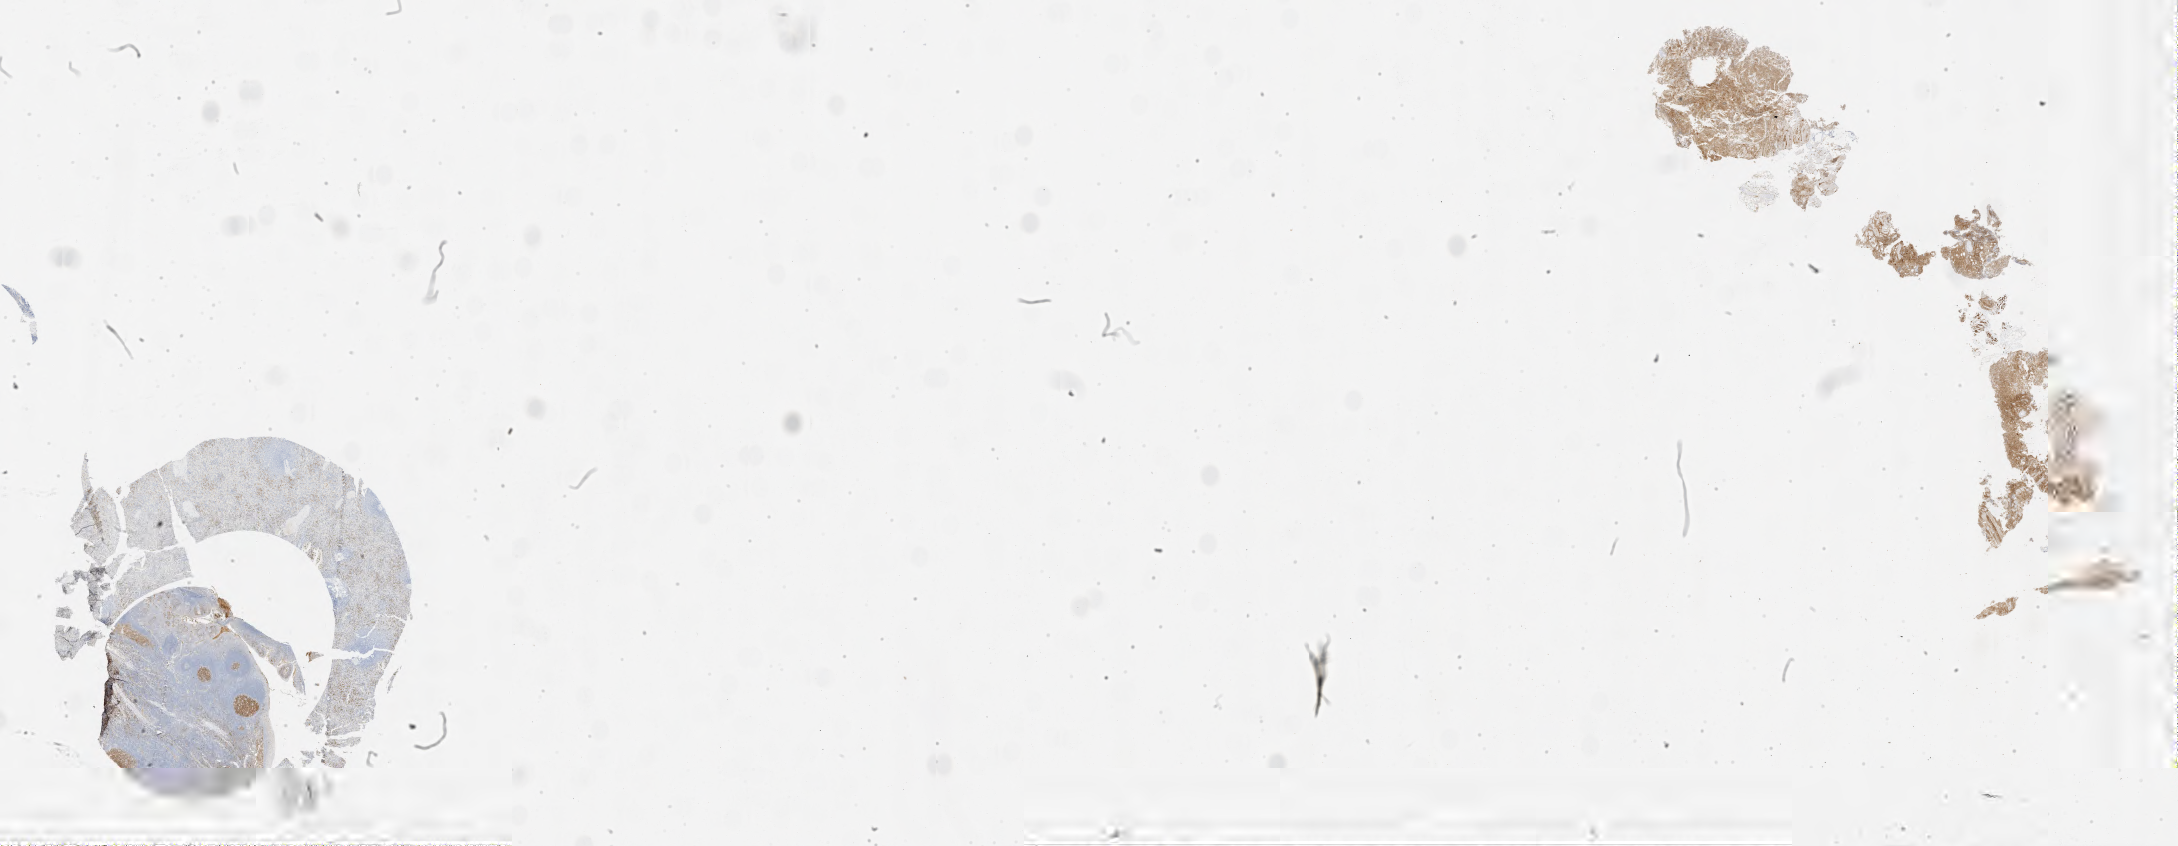
Whole-slide image, immunohistochemical stain for CD10 — whole scanned area (about 35.0 x 13.6 mm) shown as a low-resolution overview, specimen: tumor tissue. Patient: female, 69 years old.
Histologic diagnosis: Burkitt lymphoma, NOS.